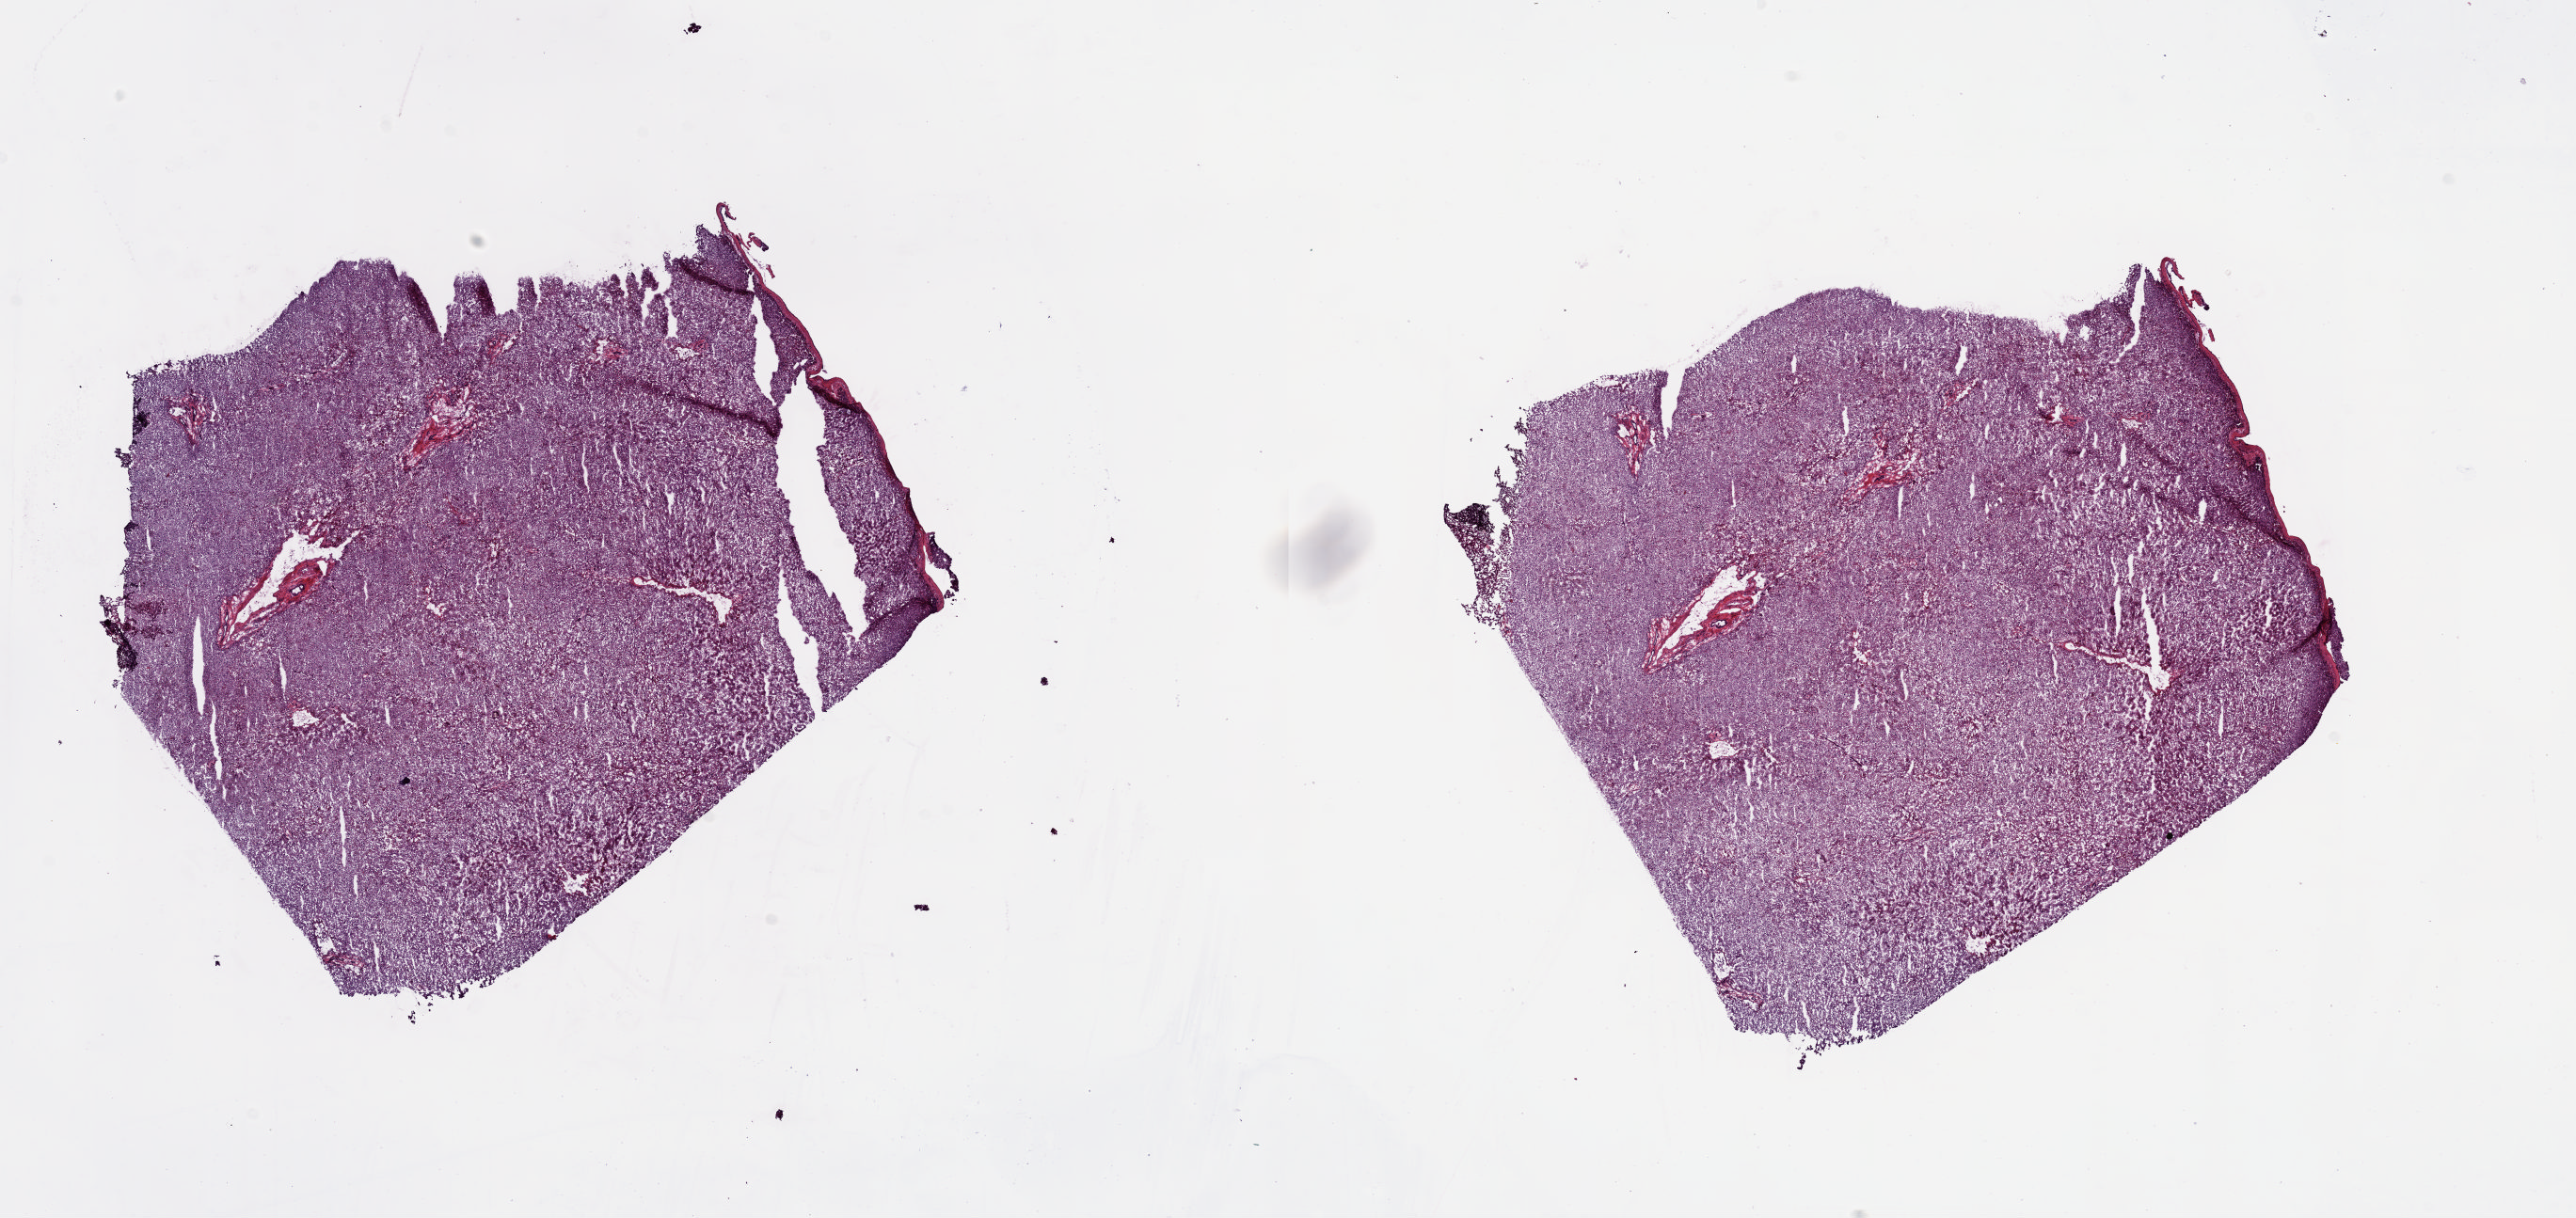
Whole-slide histology image, Hematoxylin and eosin (H&E) stained — shown as a low-resolution overview of the whole scanned area (about 21.6 x 10.2 mm), frozen section, sample: solid tissue normal (non-tumour tissue), liver. Female patient; age at initial diagnosis 61 years. Slide review estimates, as recorded: tumour cells 0%, tumour nuclei 0%, normal cells 100%, stromal cells 0%, necrosis 0%. Infiltration values recorded for this section: lymphocyte infiltration 3%, monocyte infiltration 0%, neutrophil infiltration 5%.
• this section: solid tissue normal sample (biorepository sample class)
• patient diagnosis: Hepatocellular carcinoma, NOS